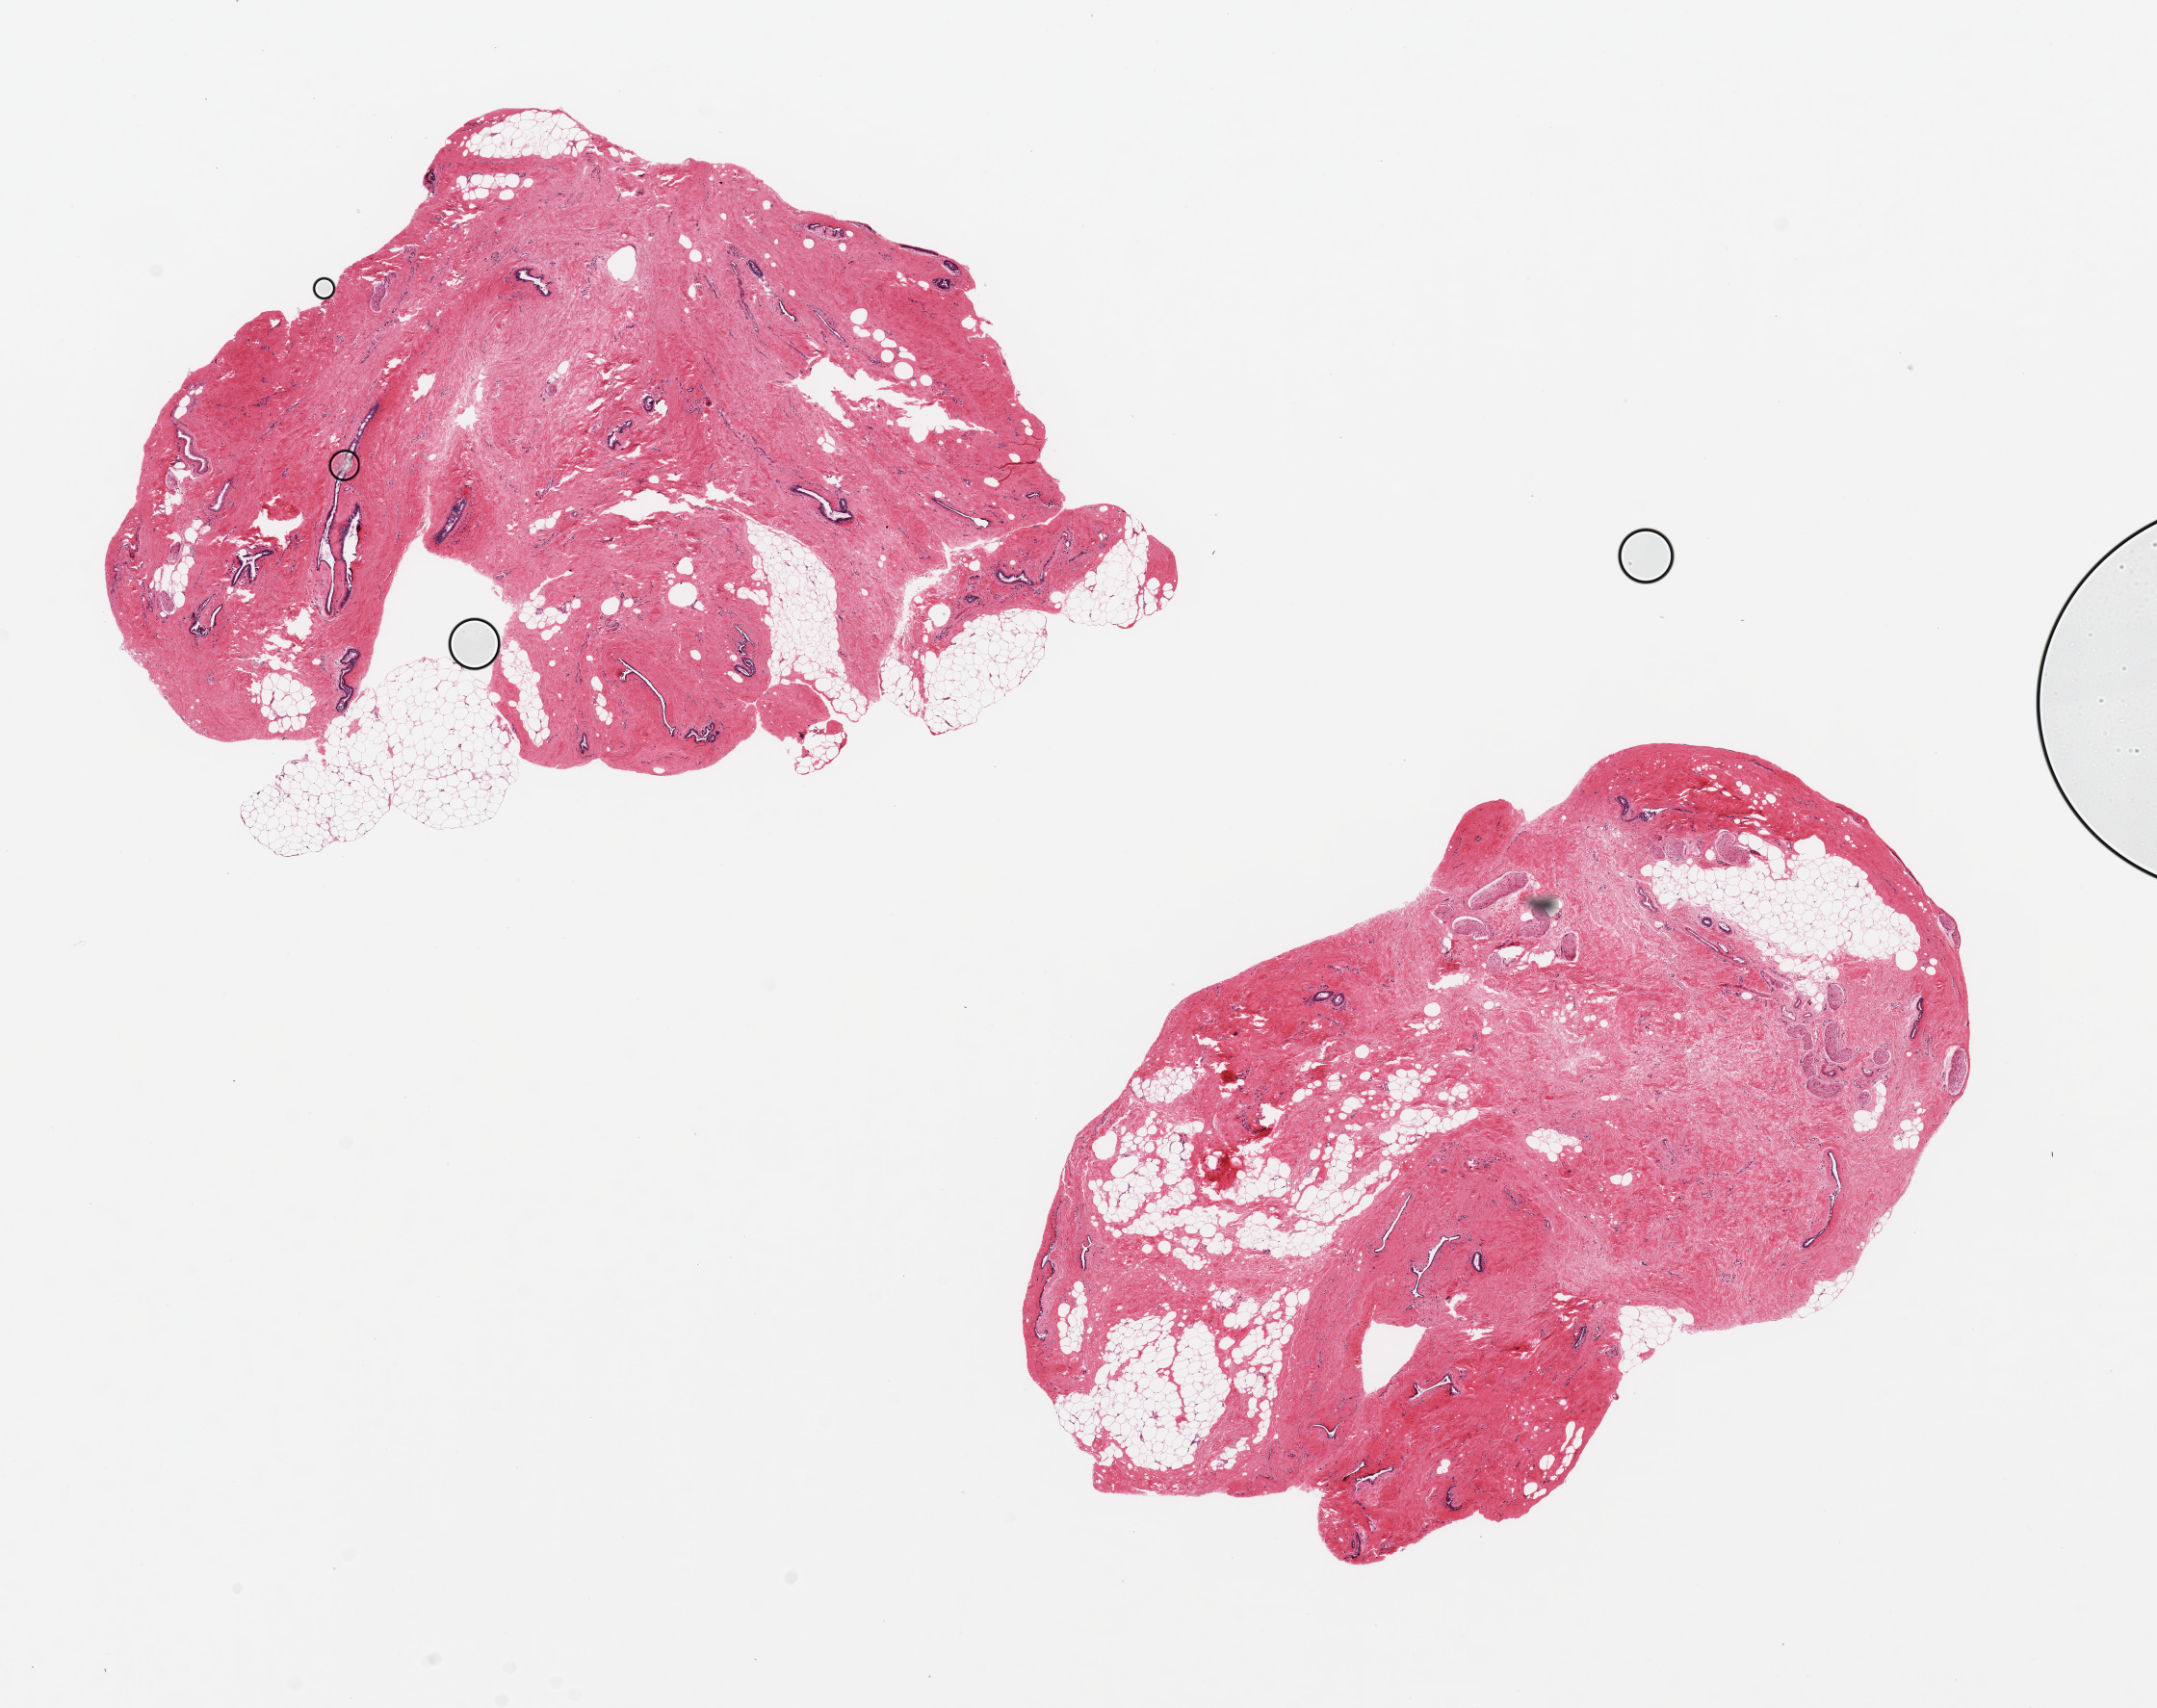
Whole-slide image, hematoxylin and eosin (H&E) stain — whole scanned area (about 17.7 x 14.0 mm, slide scanned at 20x) shown as a low-resolution overview; PAXgene-fixed, paraffin-embedded tissue; sampled site (target tissue): breast; tissue donor sample. Donor: male.
• review note (as recorded): 2 pieces ~8x6mm; Ductal elements present, mild gynecomastic hyperplastic changes noted